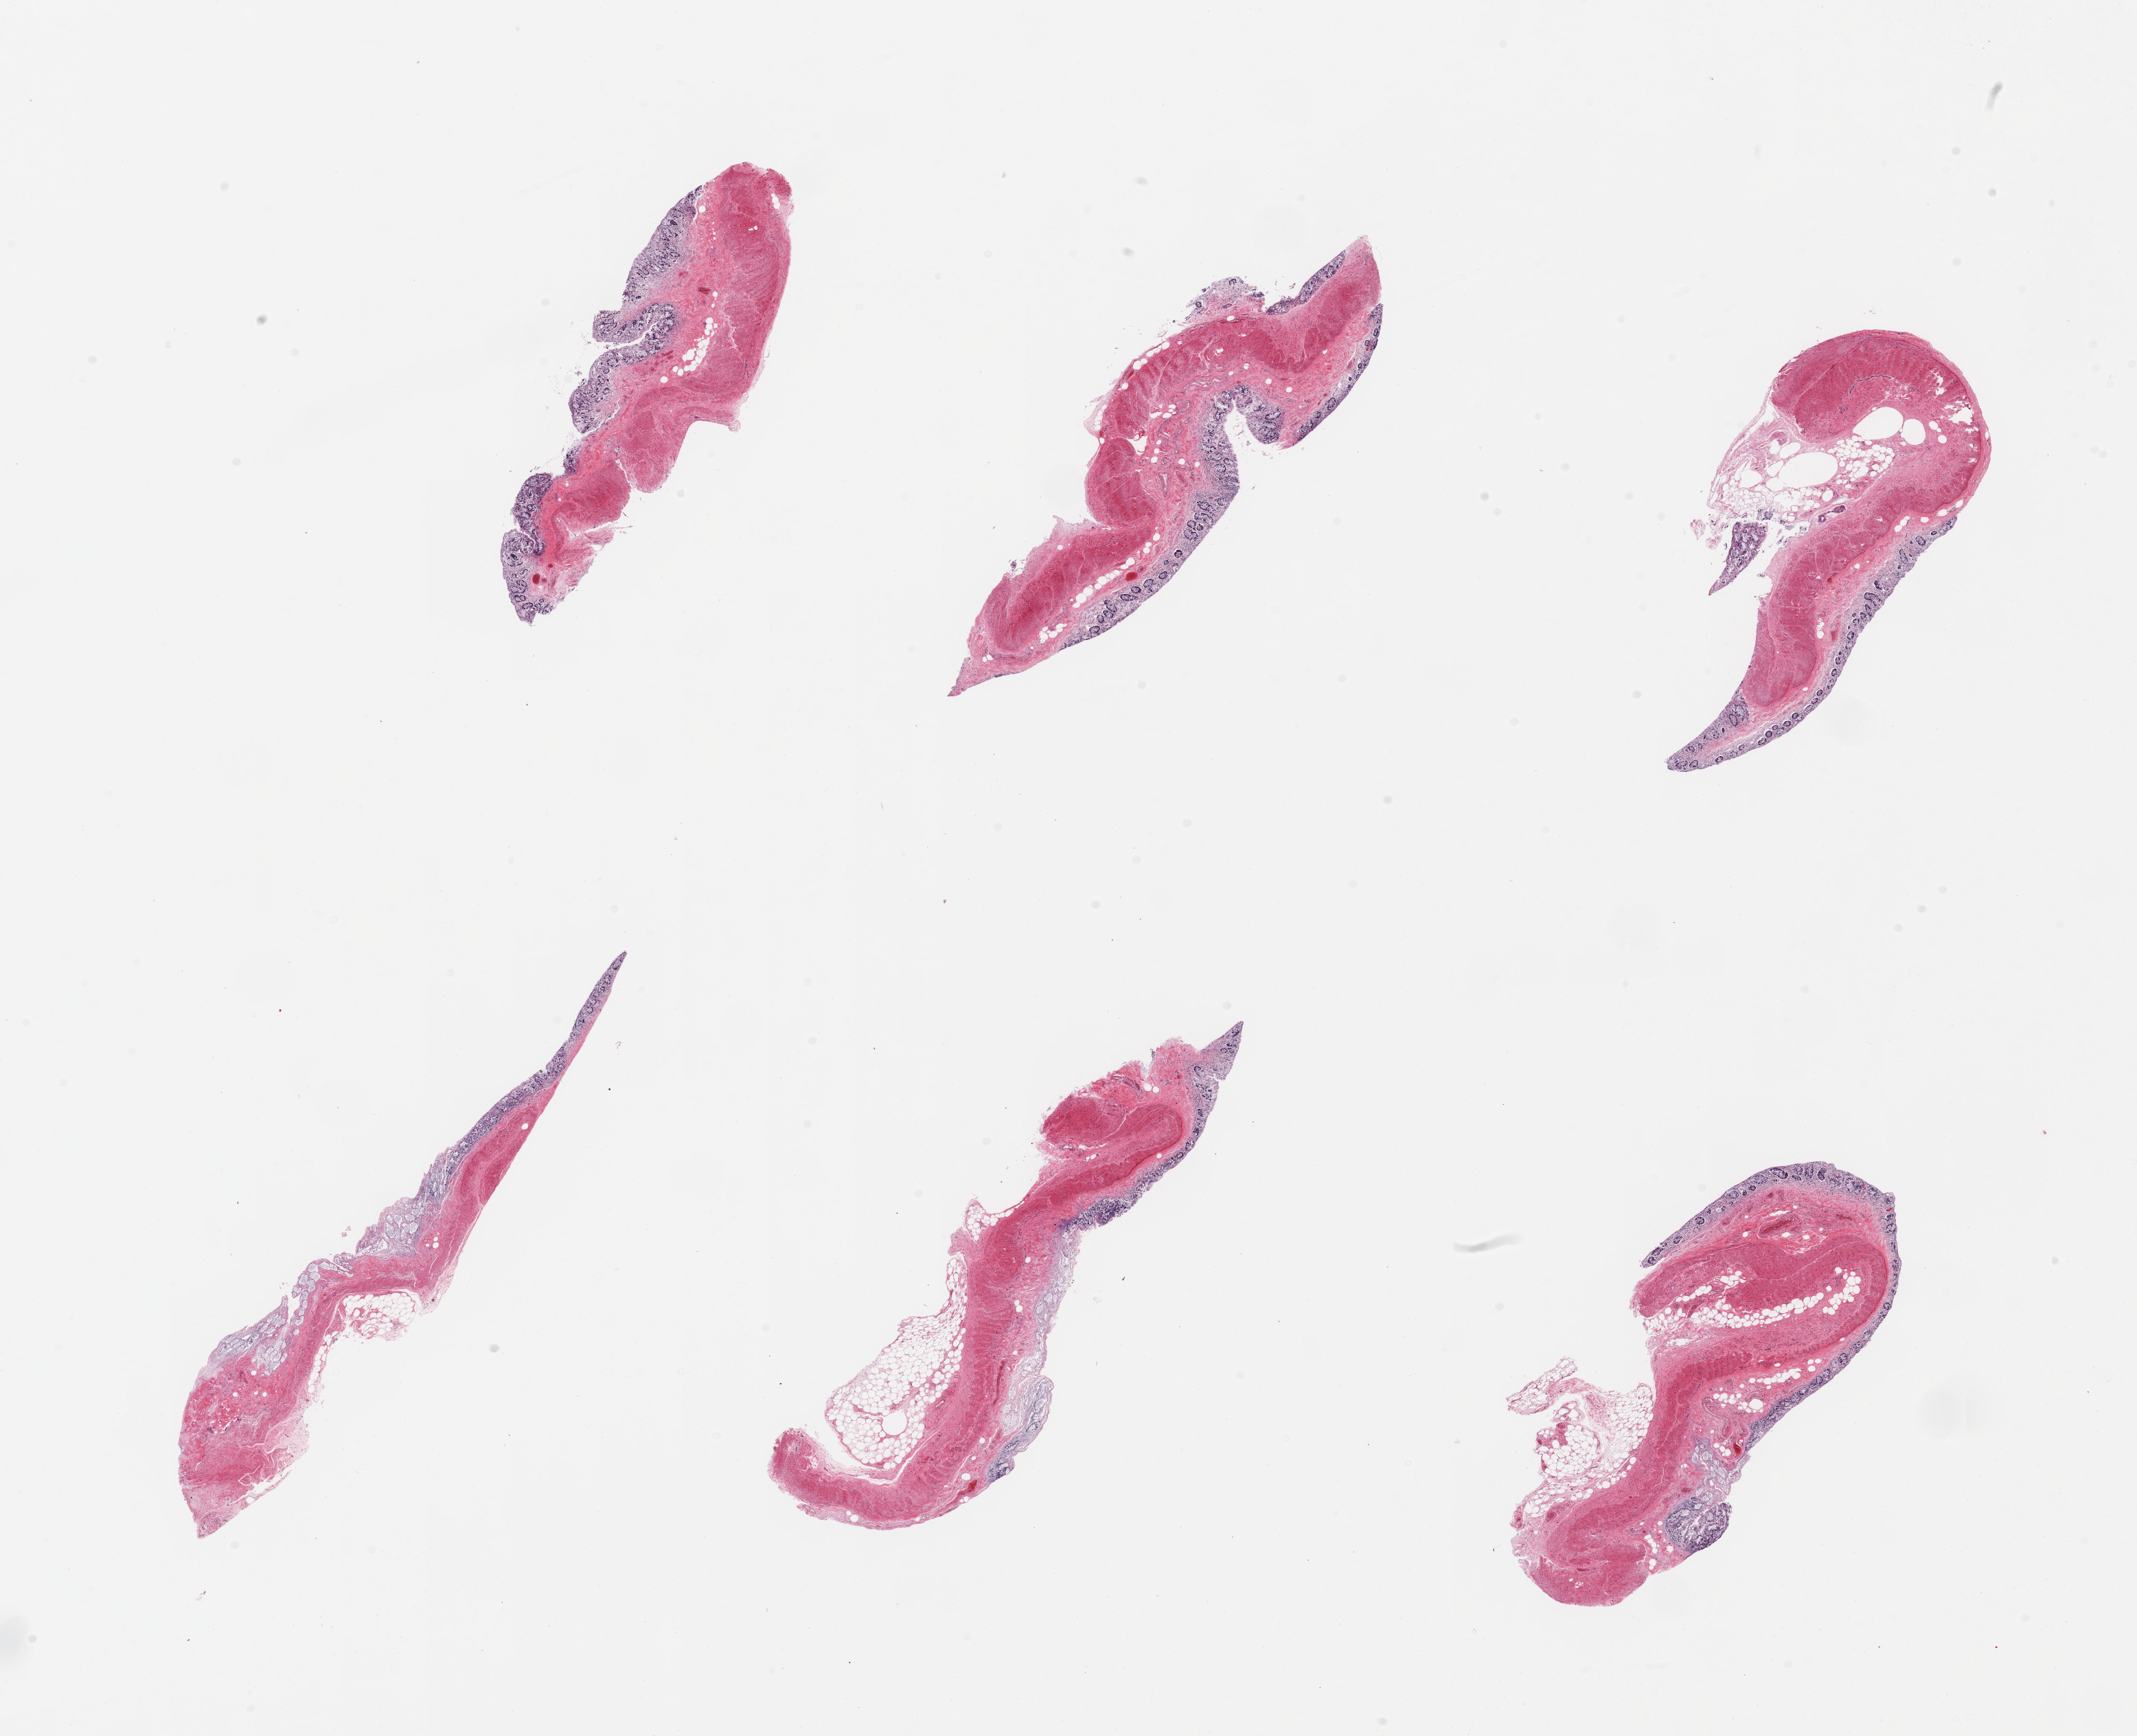
Digitized hematoxylin and eosin (H&E)-stained section — a low-resolution overview of the entire scanned area, about 24.6 x 20.0 mm. PAXgene-fixed, paraffin-embedded tissue. Target tissue: transverse colon. Donor tissue sample. Donor sex: female.
Pathologist's review note for this sample: 6 pieces, mucosa up to ~0.3mm, but with advanced autolysis, loss of glandular elements.